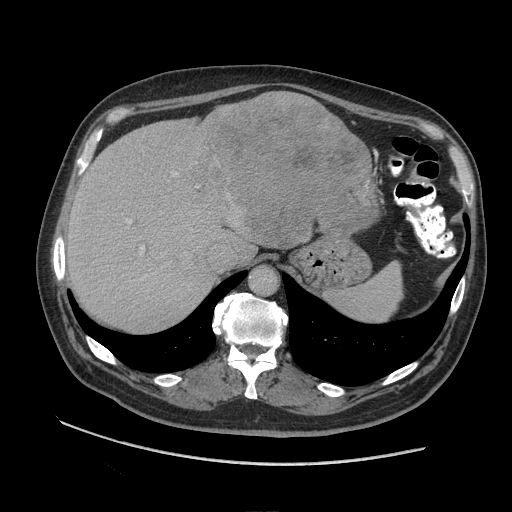
Contrast-enhanced abdominal CT (liver protocol), one axial slice; position 71 of 109 along the scan axis; 140 kVp; soft-tissue window (W 400 / L 40 HU); 512 × 512 image matrix, field of view 420 × 420 mm. Case-level facts recorded for this patient, not image findings: diagnosis: hepatocellular carcinoma (patient treated with transarterial chemoembolisation; whether this scan precedes or follows treatment is not stated here); TNM stage (as recorded): Stage-I; Child-Pugh class: A; tumour nodularity: uninodular.
Outlined on this slice (semi-automatically segmented with operator editing):
- abdominal aorta: bounding box <250,268,277,296> (left, top, right, bottom; pixels)
- liver parenchyma outside the tumour (the mass and vessels are separate outlines, so this box may not span the whole liver): <66,92,372,330>
- mass: <198,91,379,248>
- liver vessels: <128,172,178,280>